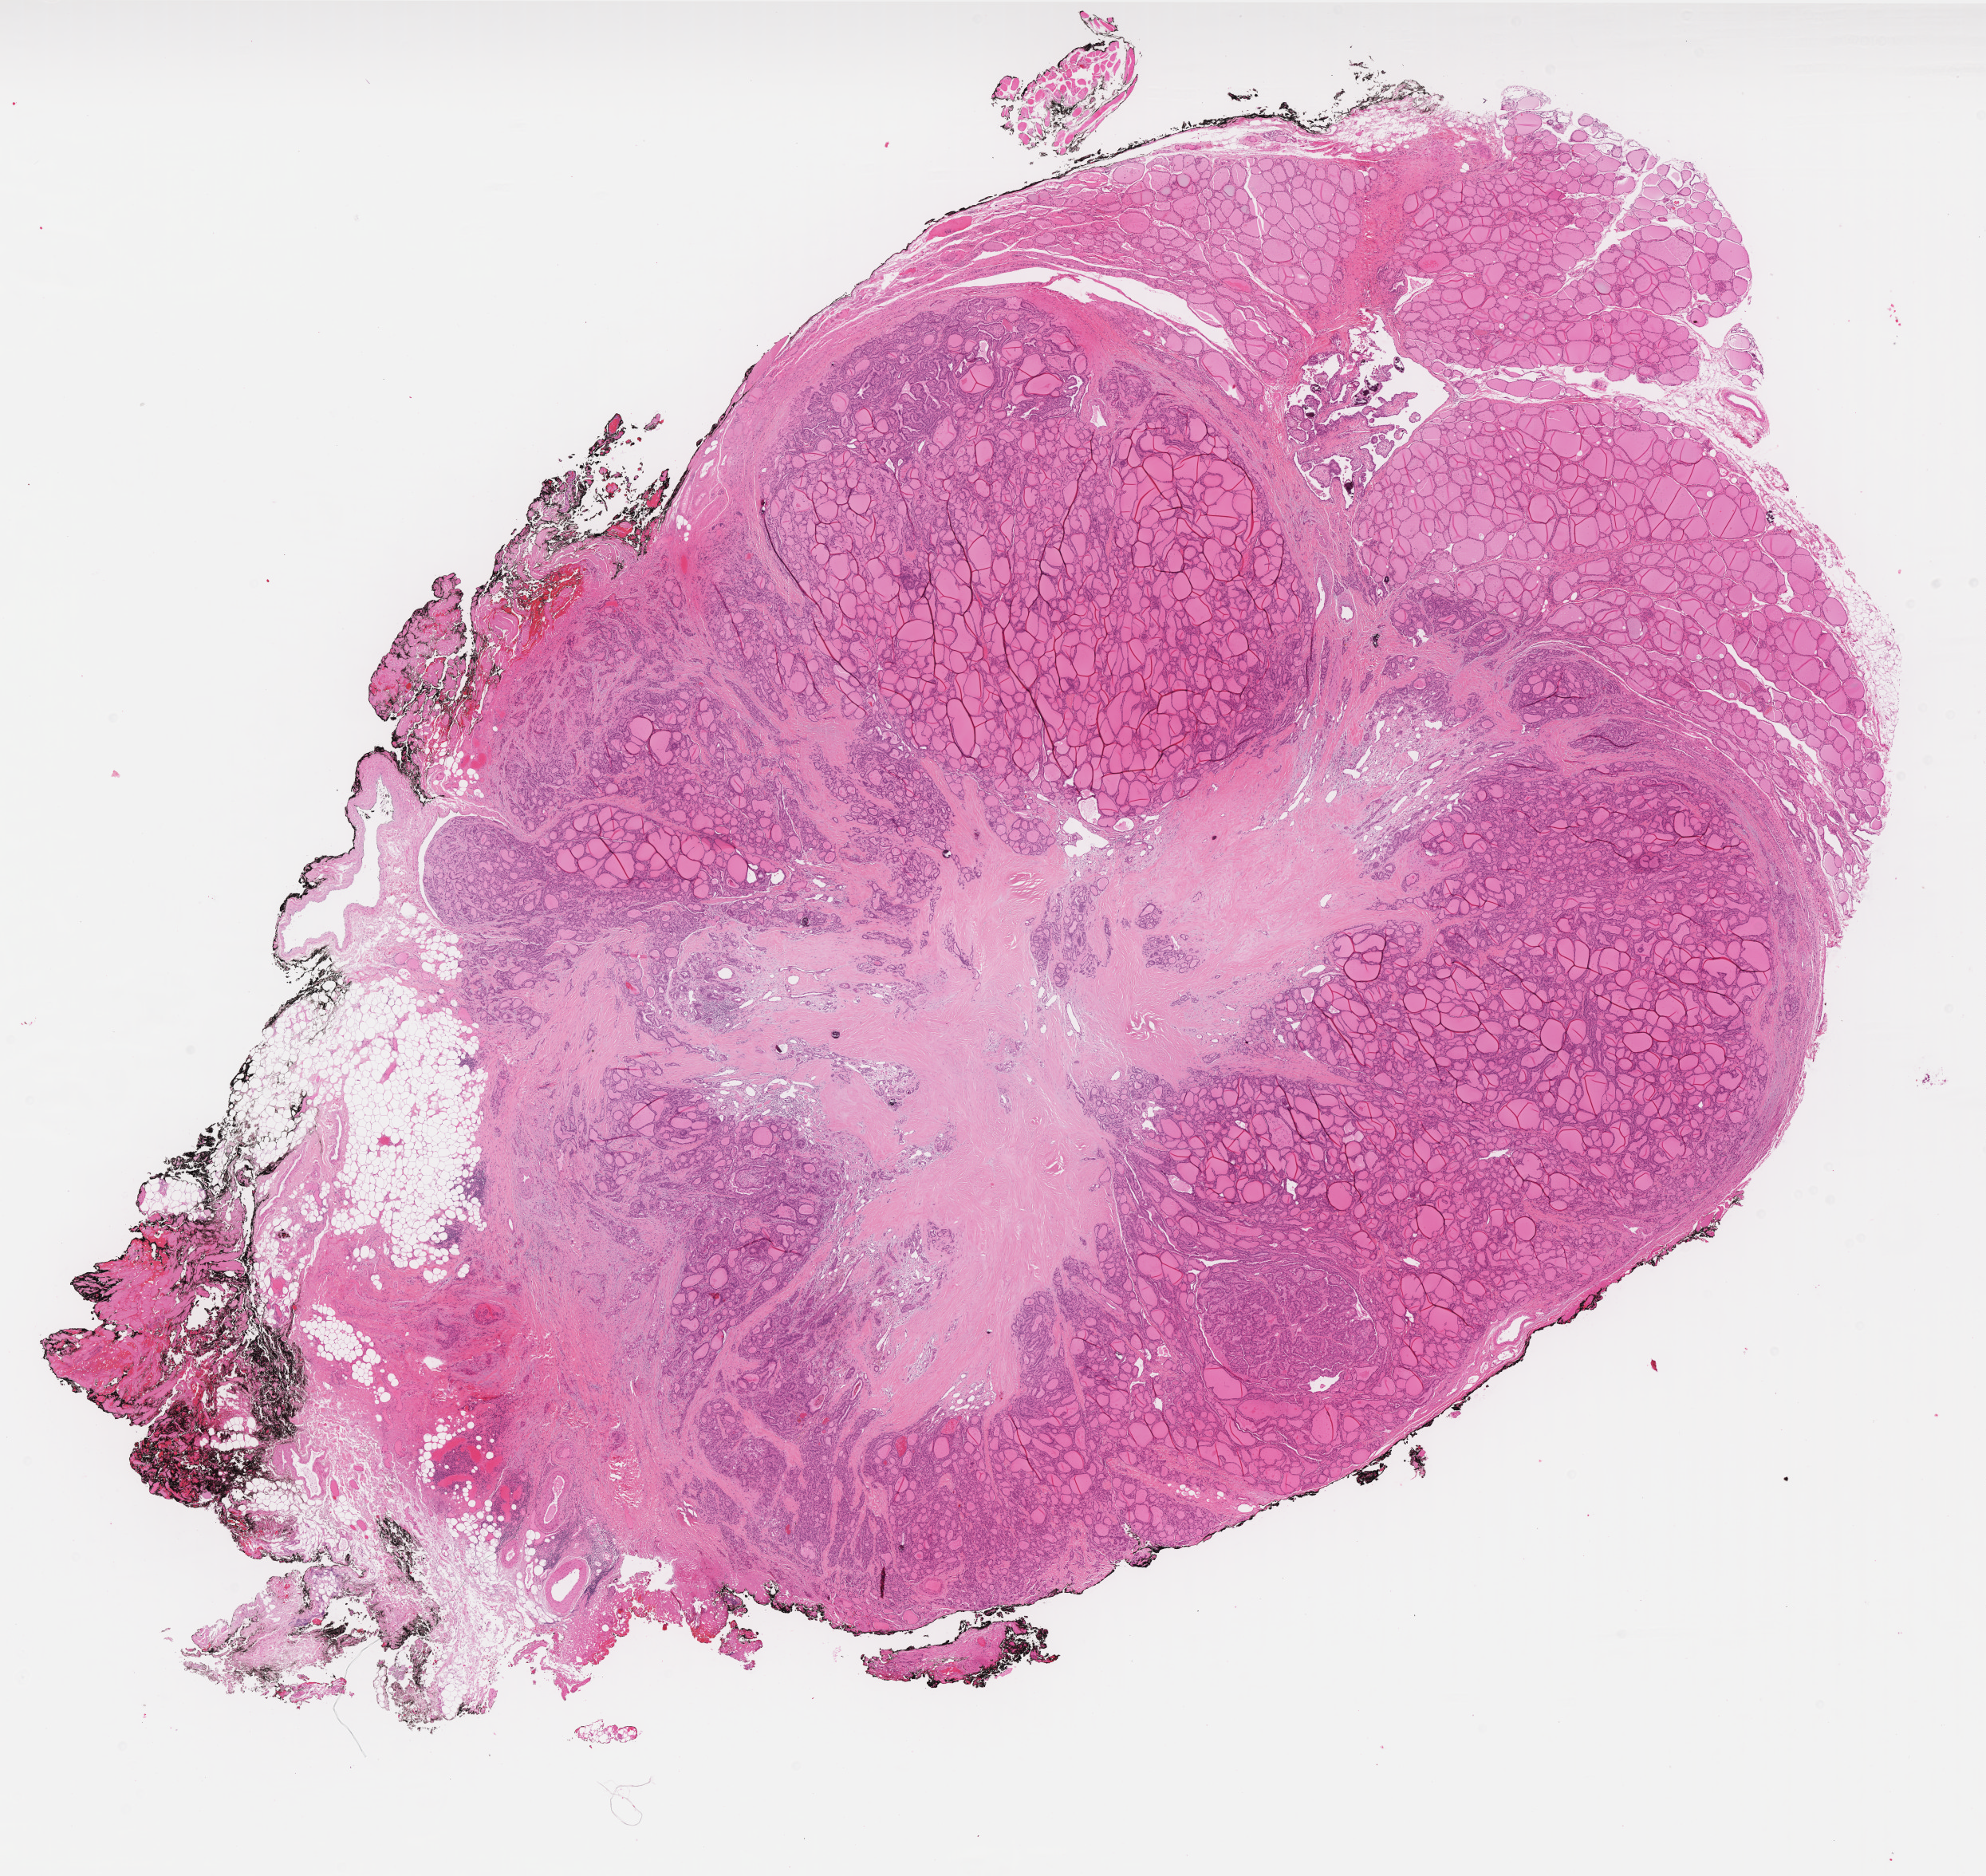
Digitized H&E tissue section (whole slide) — a low-resolution overview of the entire scanned area, about 20.0 x 18.9 mm, formalin-fixed paraffin-embedded (FFPE) diagnostic section, thyroid, primary tumour sample. Patient: male, age at initial diagnosis 45 years.
* AJCC pathologic stage: III (7th edition)
* diagnosis: Papillary adenocarcinoma, NOS
* lymph nodes positive (case pathology): 1 of 1 examined
* laterality: bilateral